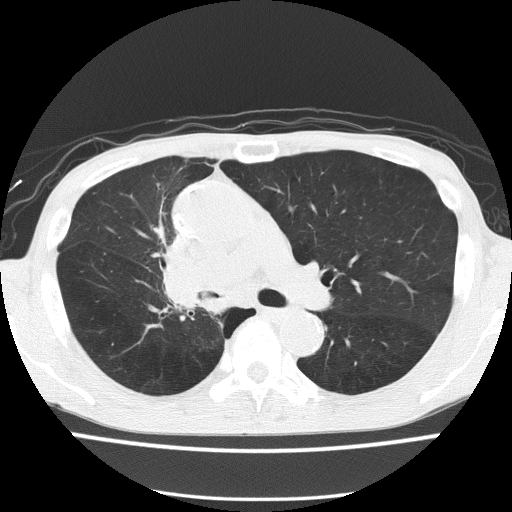
Low-dose screening chest CT, axial slice; baseline screening round; lung window (W 1500 / L -600 HU); slice 58 of 150 in the series. Male participant, aged 59 years at enrolment. Former smoker at enrolment.
- Expert-annotated lung lesion, box from (x=142, y=229) to (x=231, y=320) px.
- The screening reader recorded 5 non-calcified nodules or masses ≥4 mm on this exam (left upper lobe, left upper lobe, left upper lobe, right middle lobe, right lower lobe); which of them this box marks is not recorded.